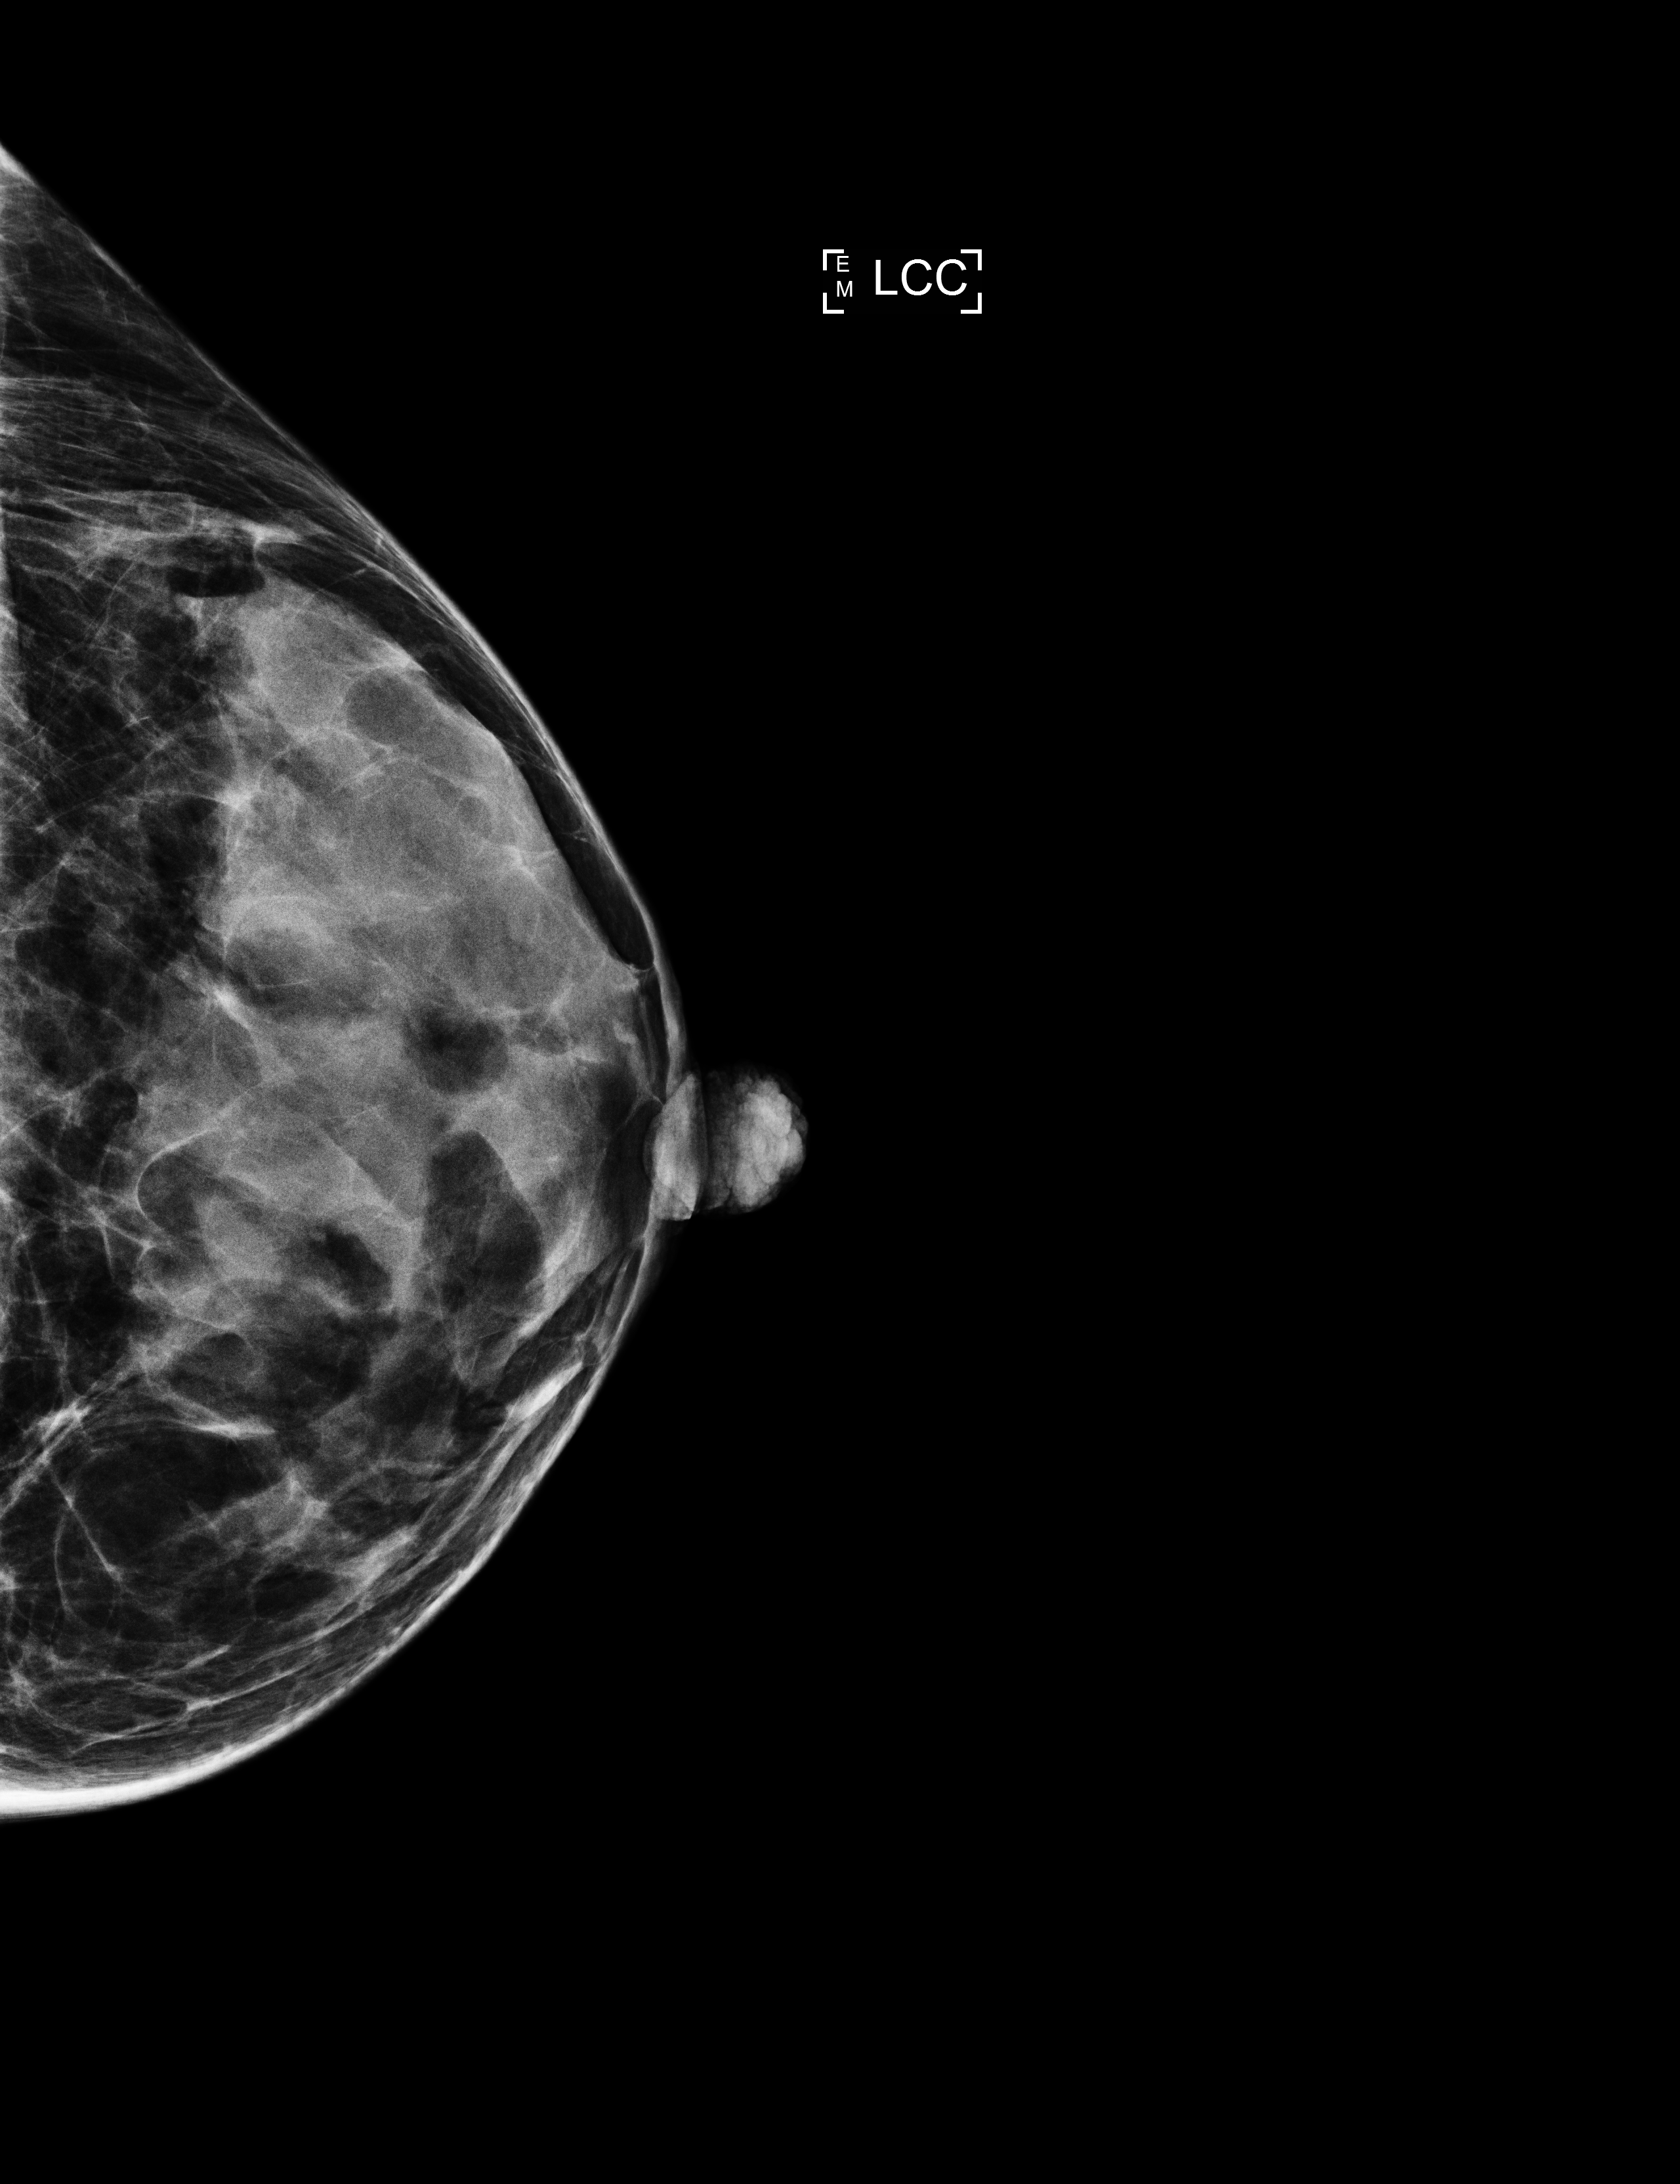
Annual screening mammography examination, compressed breast thickness 38 mm, system: Selenia Dimensions. Patient: female, 43 years.
Image type: full-field digital mammogram. Breast: left. Projection: craniocaudal (CC) view.